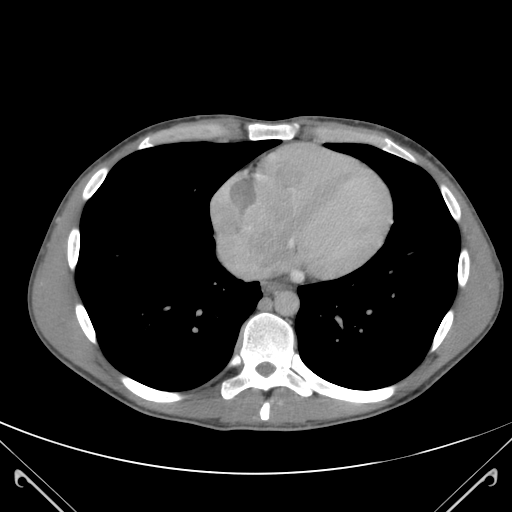
Contrast-enhanced abdominal CT (liver protocol), one axial slice; position 115 of 118 along the scan axis; soft-tissue window (W 400 / L 40 HU); 512 × 512 image matrix, field of view 380 × 380 mm. Case-level facts recorded for this patient, not image findings: diagnosis: hepatocellular carcinoma (patient treated with transarterial chemoembolisation; whether this scan precedes or follows treatment is not stated here); TNM stage (as recorded): Stage-IIIB; Child-Pugh class: A; tumour nodularity: uninodular.
Outlined on this slice (semi-automatically segmented with operator editing):
- abdominal aorta: bounding box <274,290,298,314> (left, top, right, bottom; pixels)